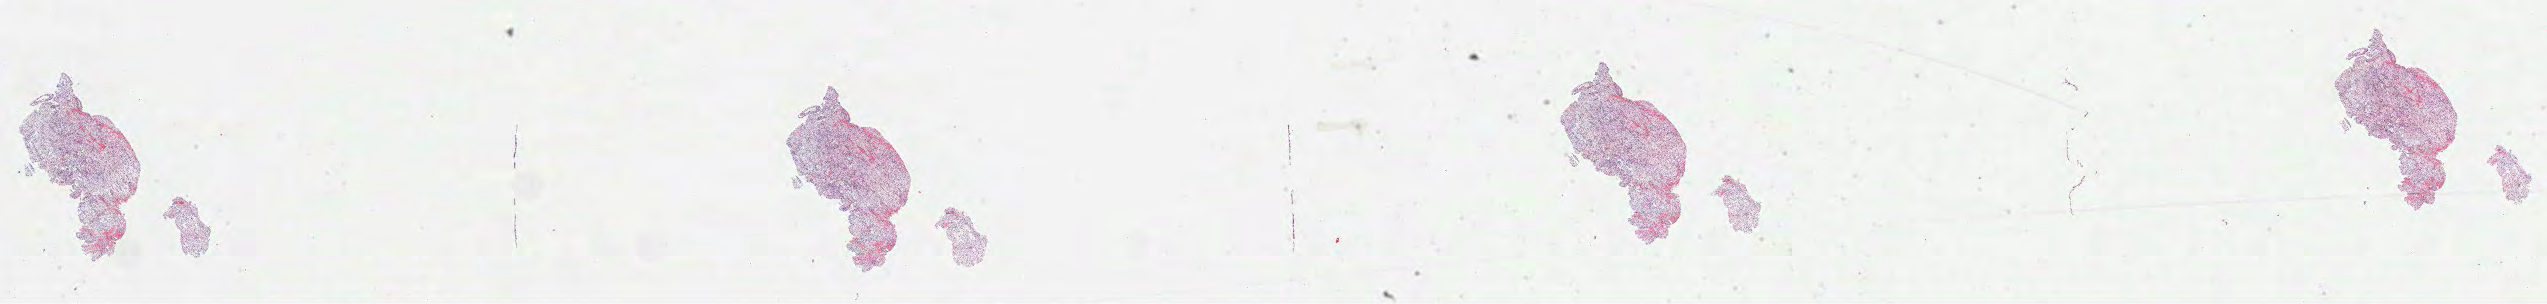
Hematoxylin and eosin (H&E) stained whole-slide image, low-resolution overview of the scanned area, about 41.1 x 4.9 mm (acquisition: 40x scan), formalin-fixed paraffin-embedded (FFPE) diagnostic section, primary tumour sample from the brain. Male patient; age at initial diagnosis 33 years.
Histologic diagnosis: Glioblastoma.